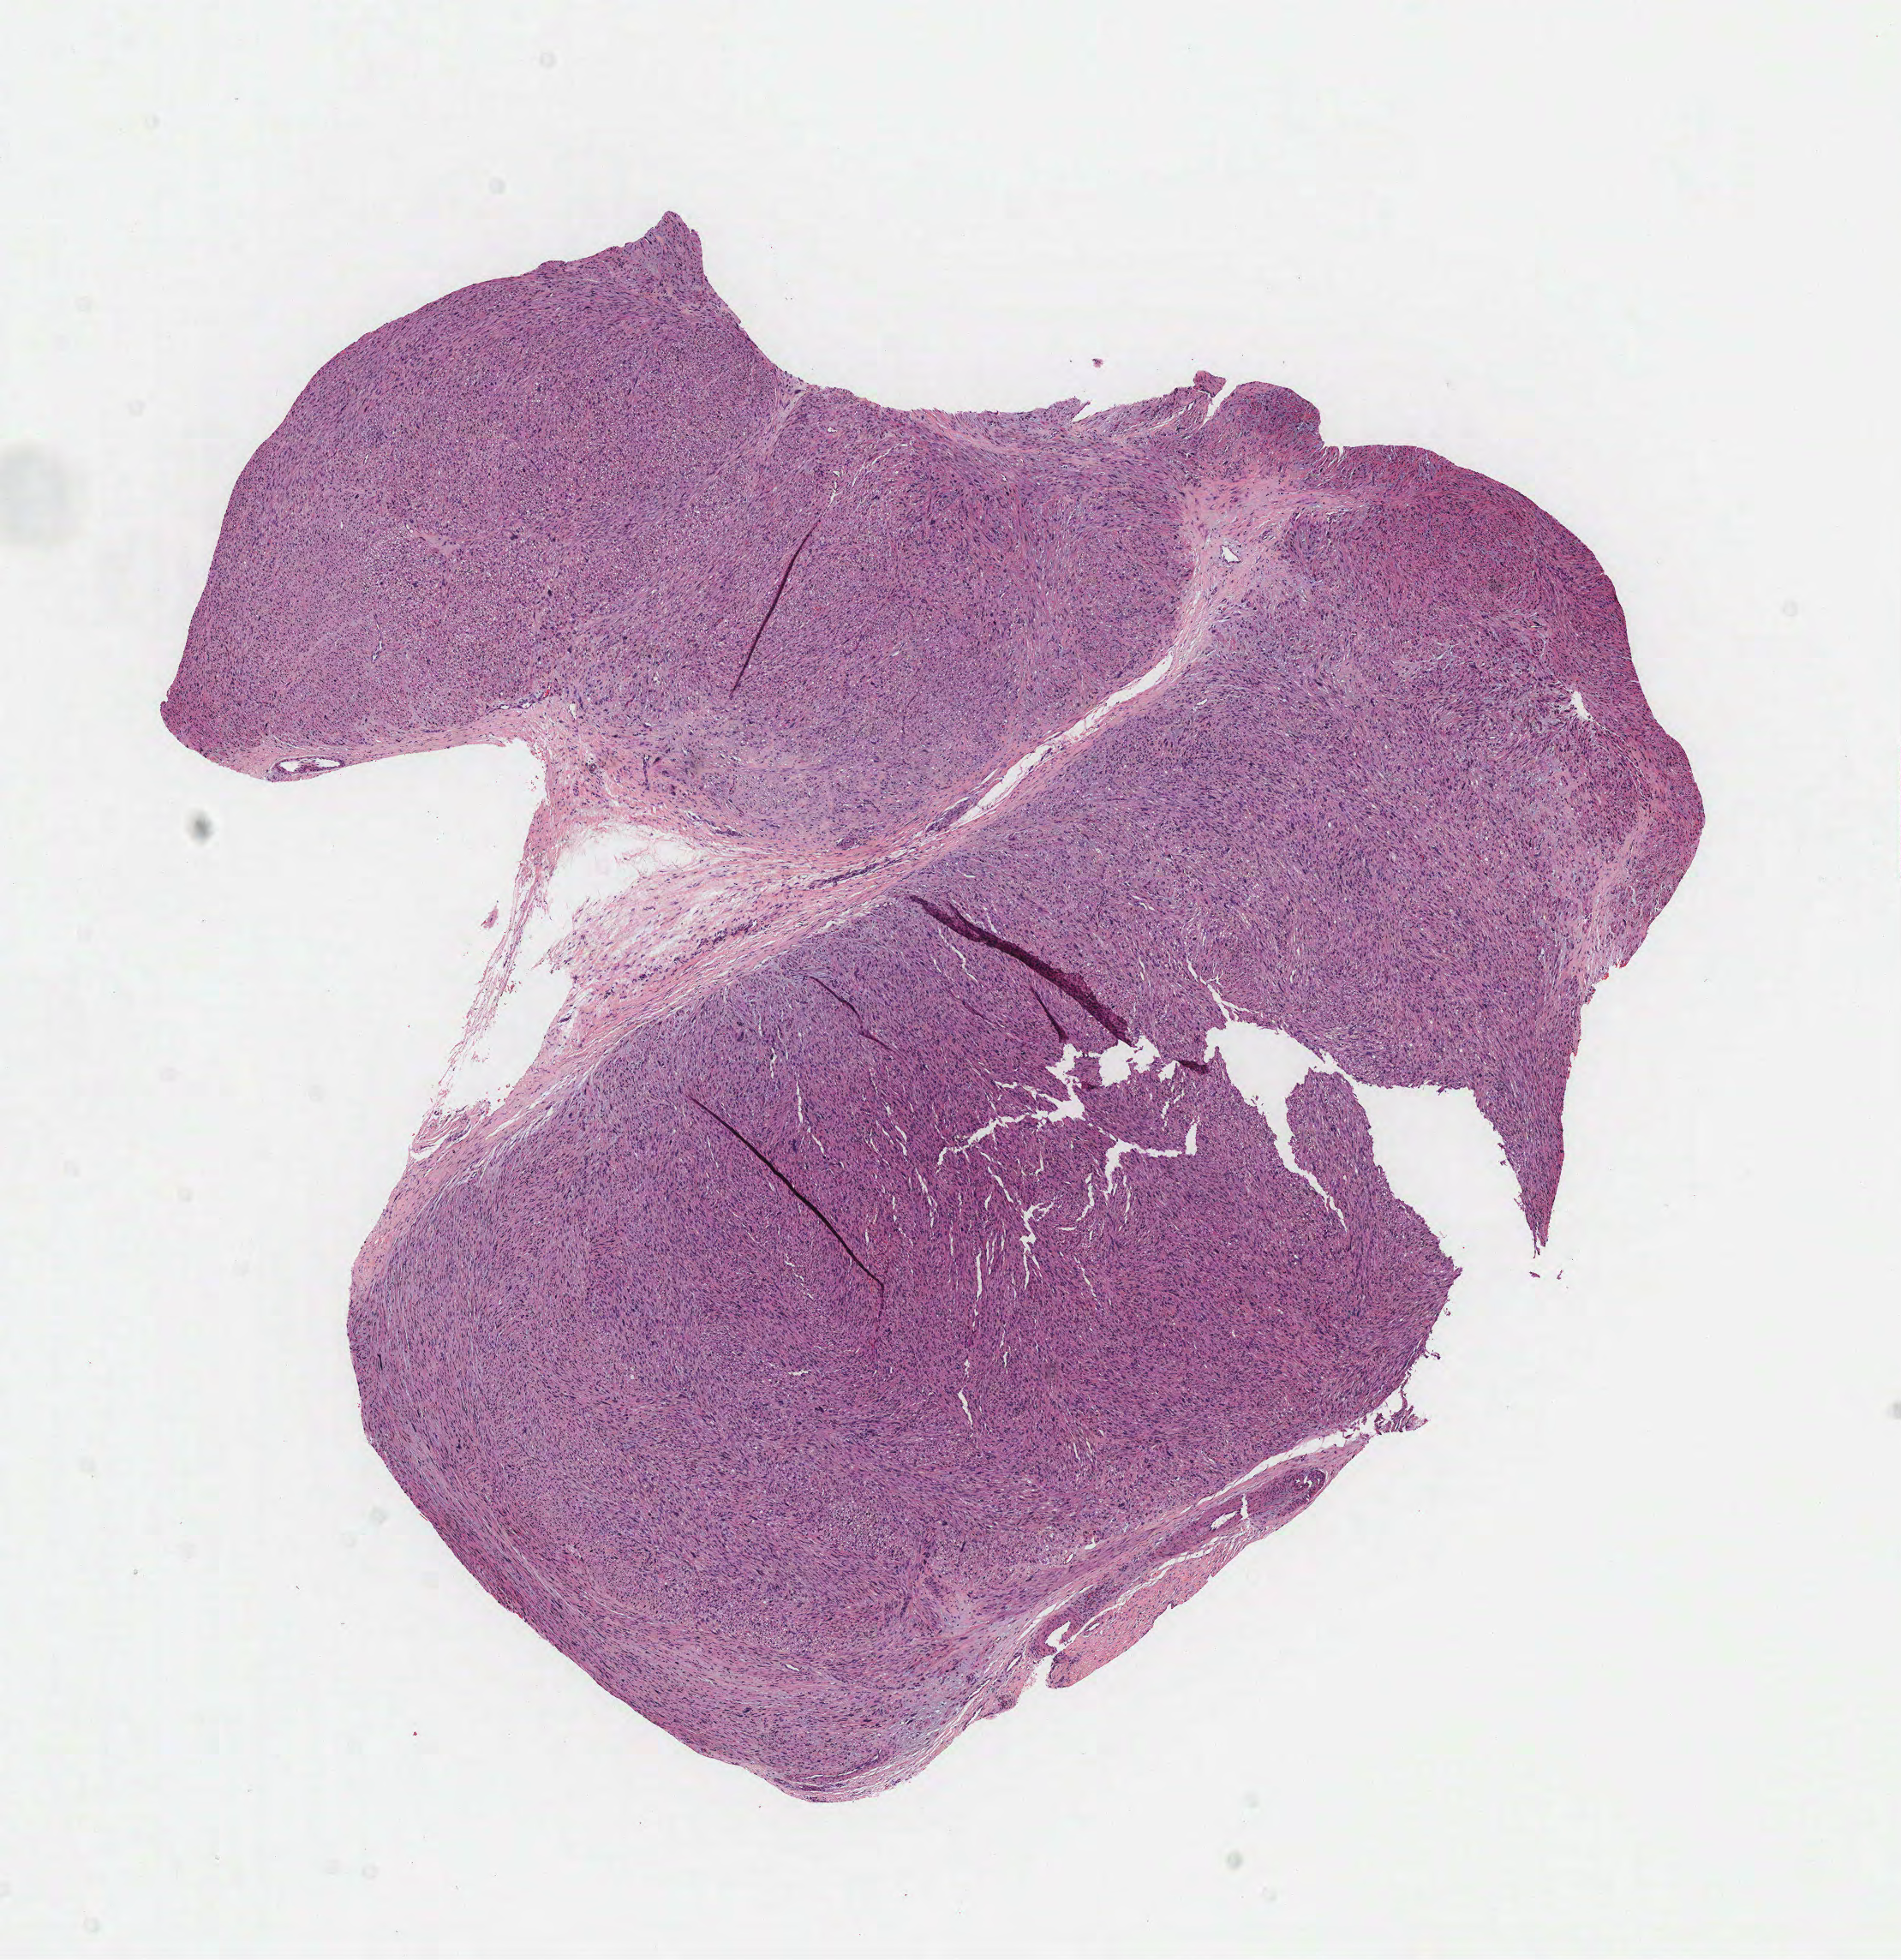
Digitized Hematoxylin and eosin (H&E) stained tissue section (whole slide), whole scanned area (about 9.0 x 9.2 mm, slide scanned at 40x) shown as a low-resolution overview, formalin-fixed paraffin-embedded (FFPE) diagnostic section, primary tumour sample from the connective, subcutaneous and other soft tissues. Patient: male, age at initial diagnosis 49 years.
Diagnosis: Leiomyosarcoma, NOS (connective, subcutaneous and other soft tissues of lower limb and hip).